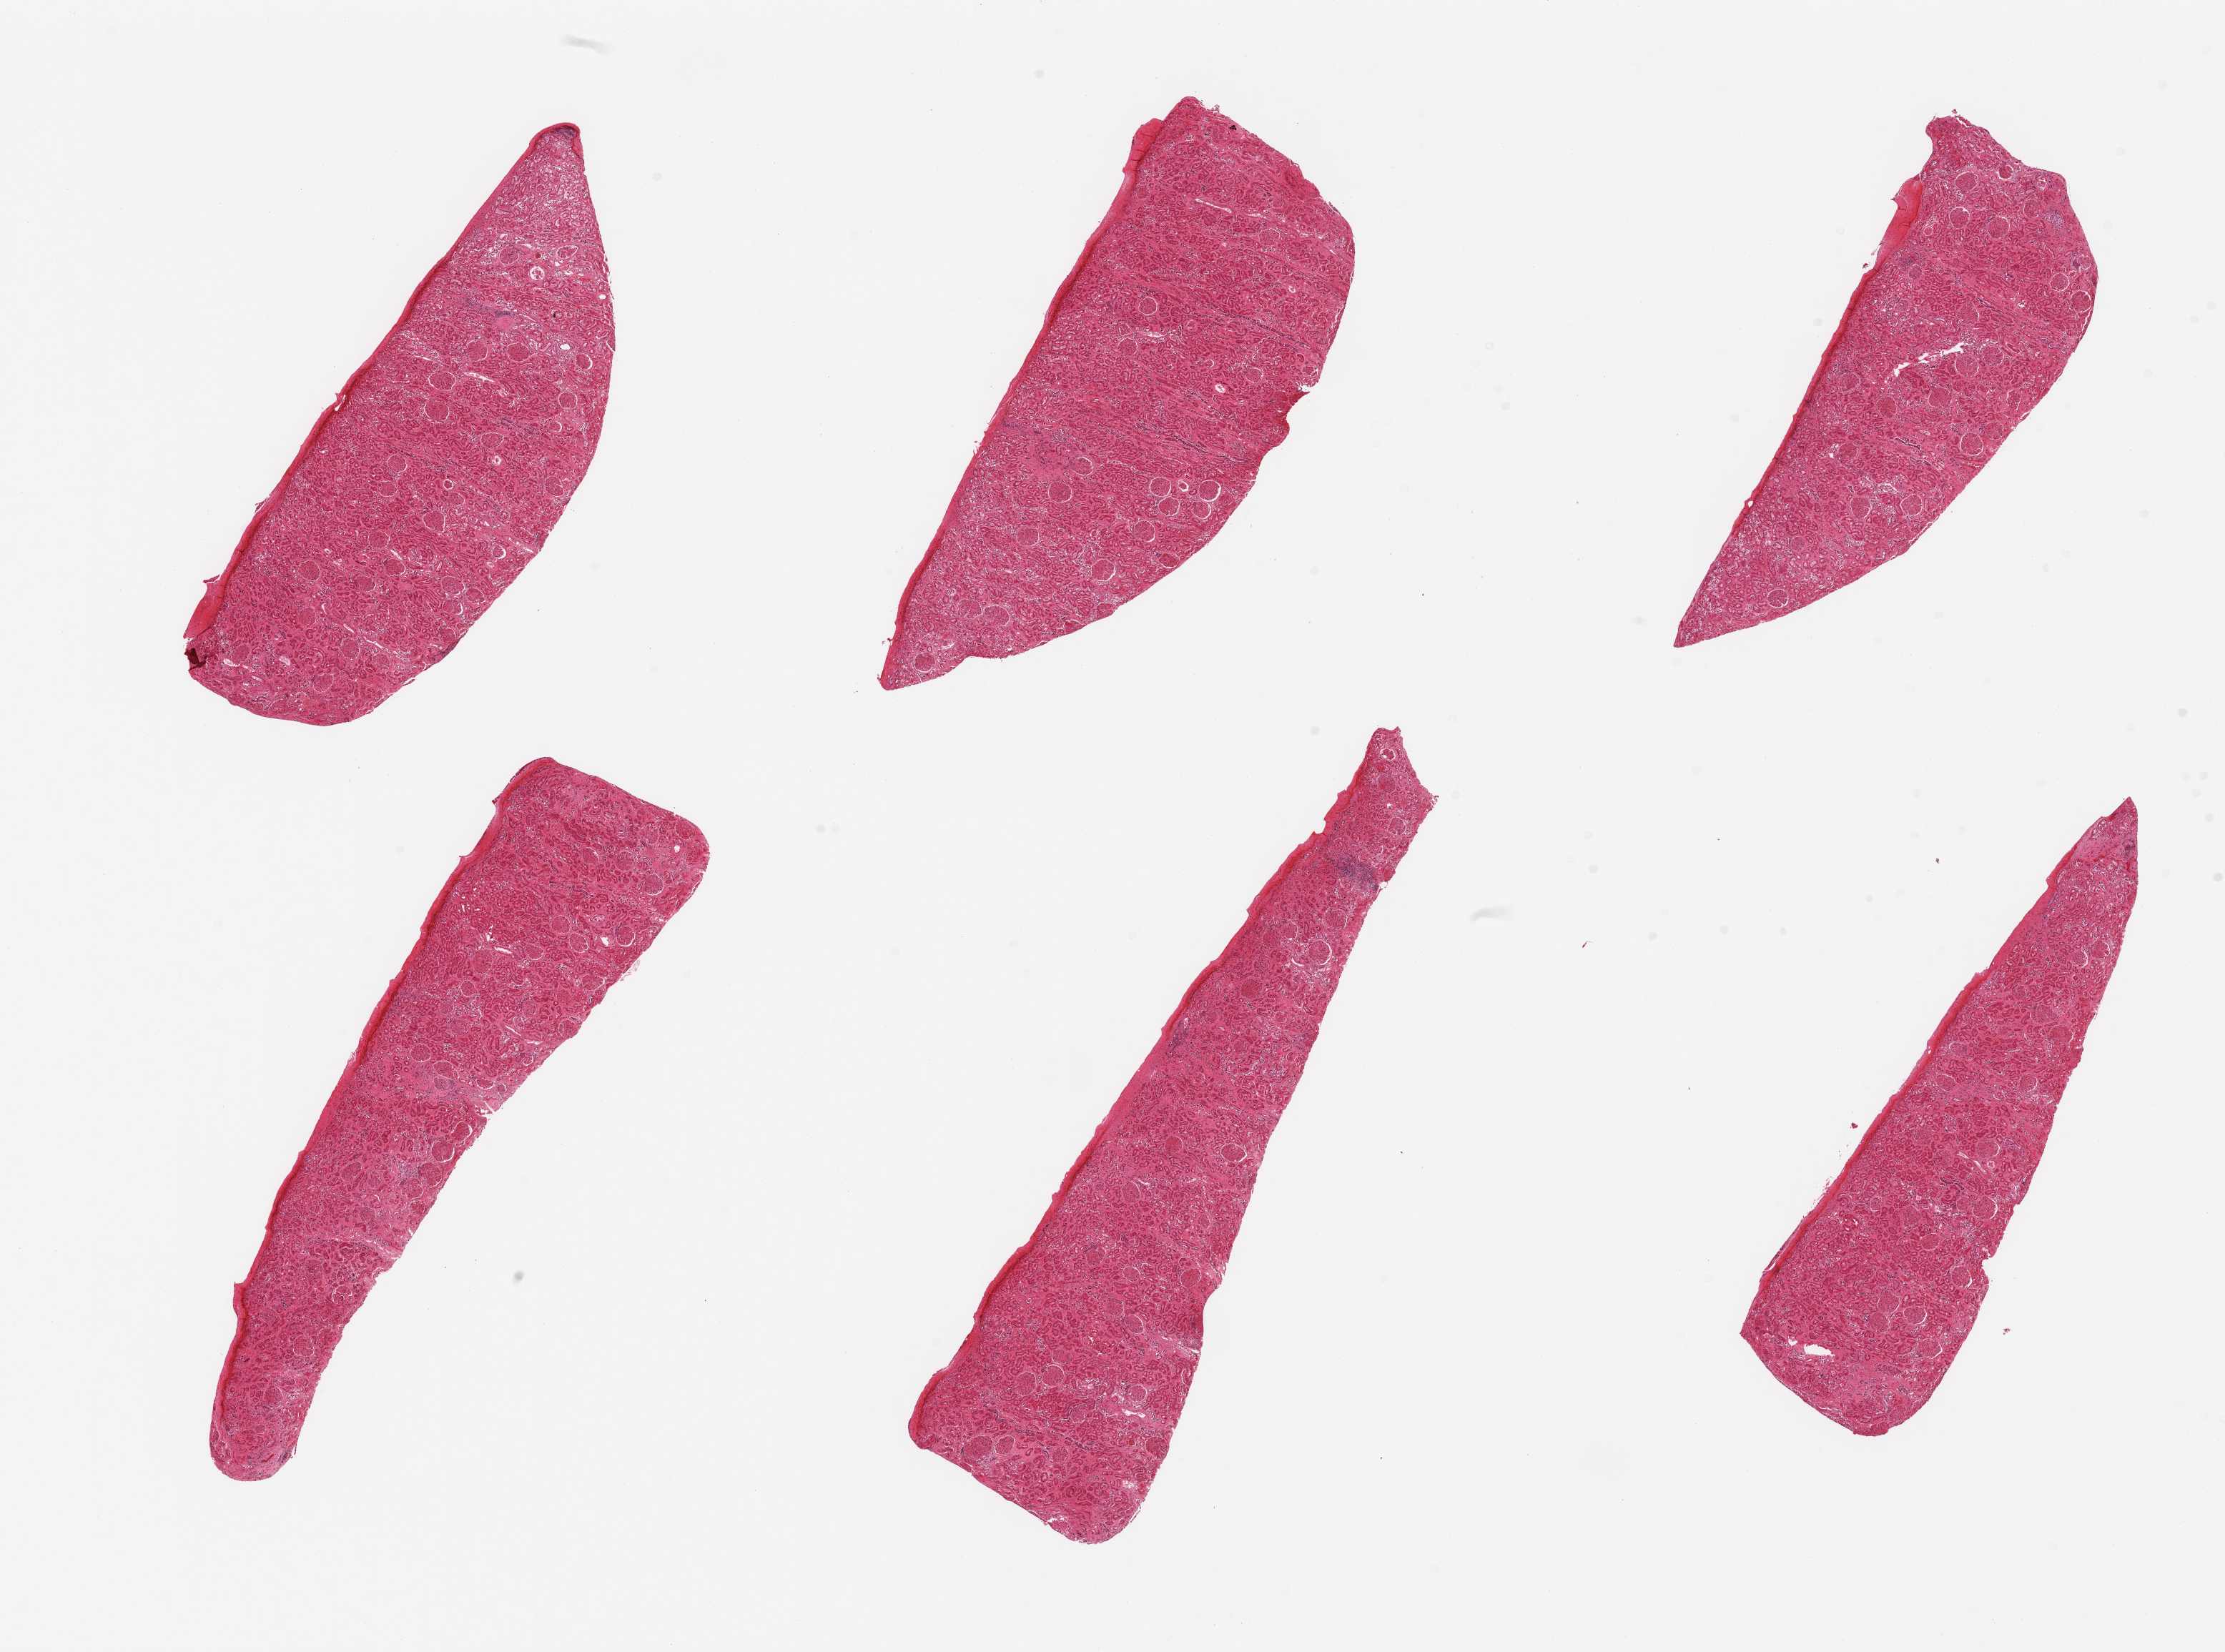
Digitized haematoxylin and eosin-stained section, brightfield, whole scanned area (about 24.6 x 18.3 mm, acquisition: 20x scan) shown as a low-resolution overview. PAXgene-fixed paraffin-embedded (PFPE) section. Target tissue: renal cortex. Tissue donor sample. Donor: male.
• reviewer comment on this tissue sample: 6 pieces, glomeruli present; tubules moderately autolyzed